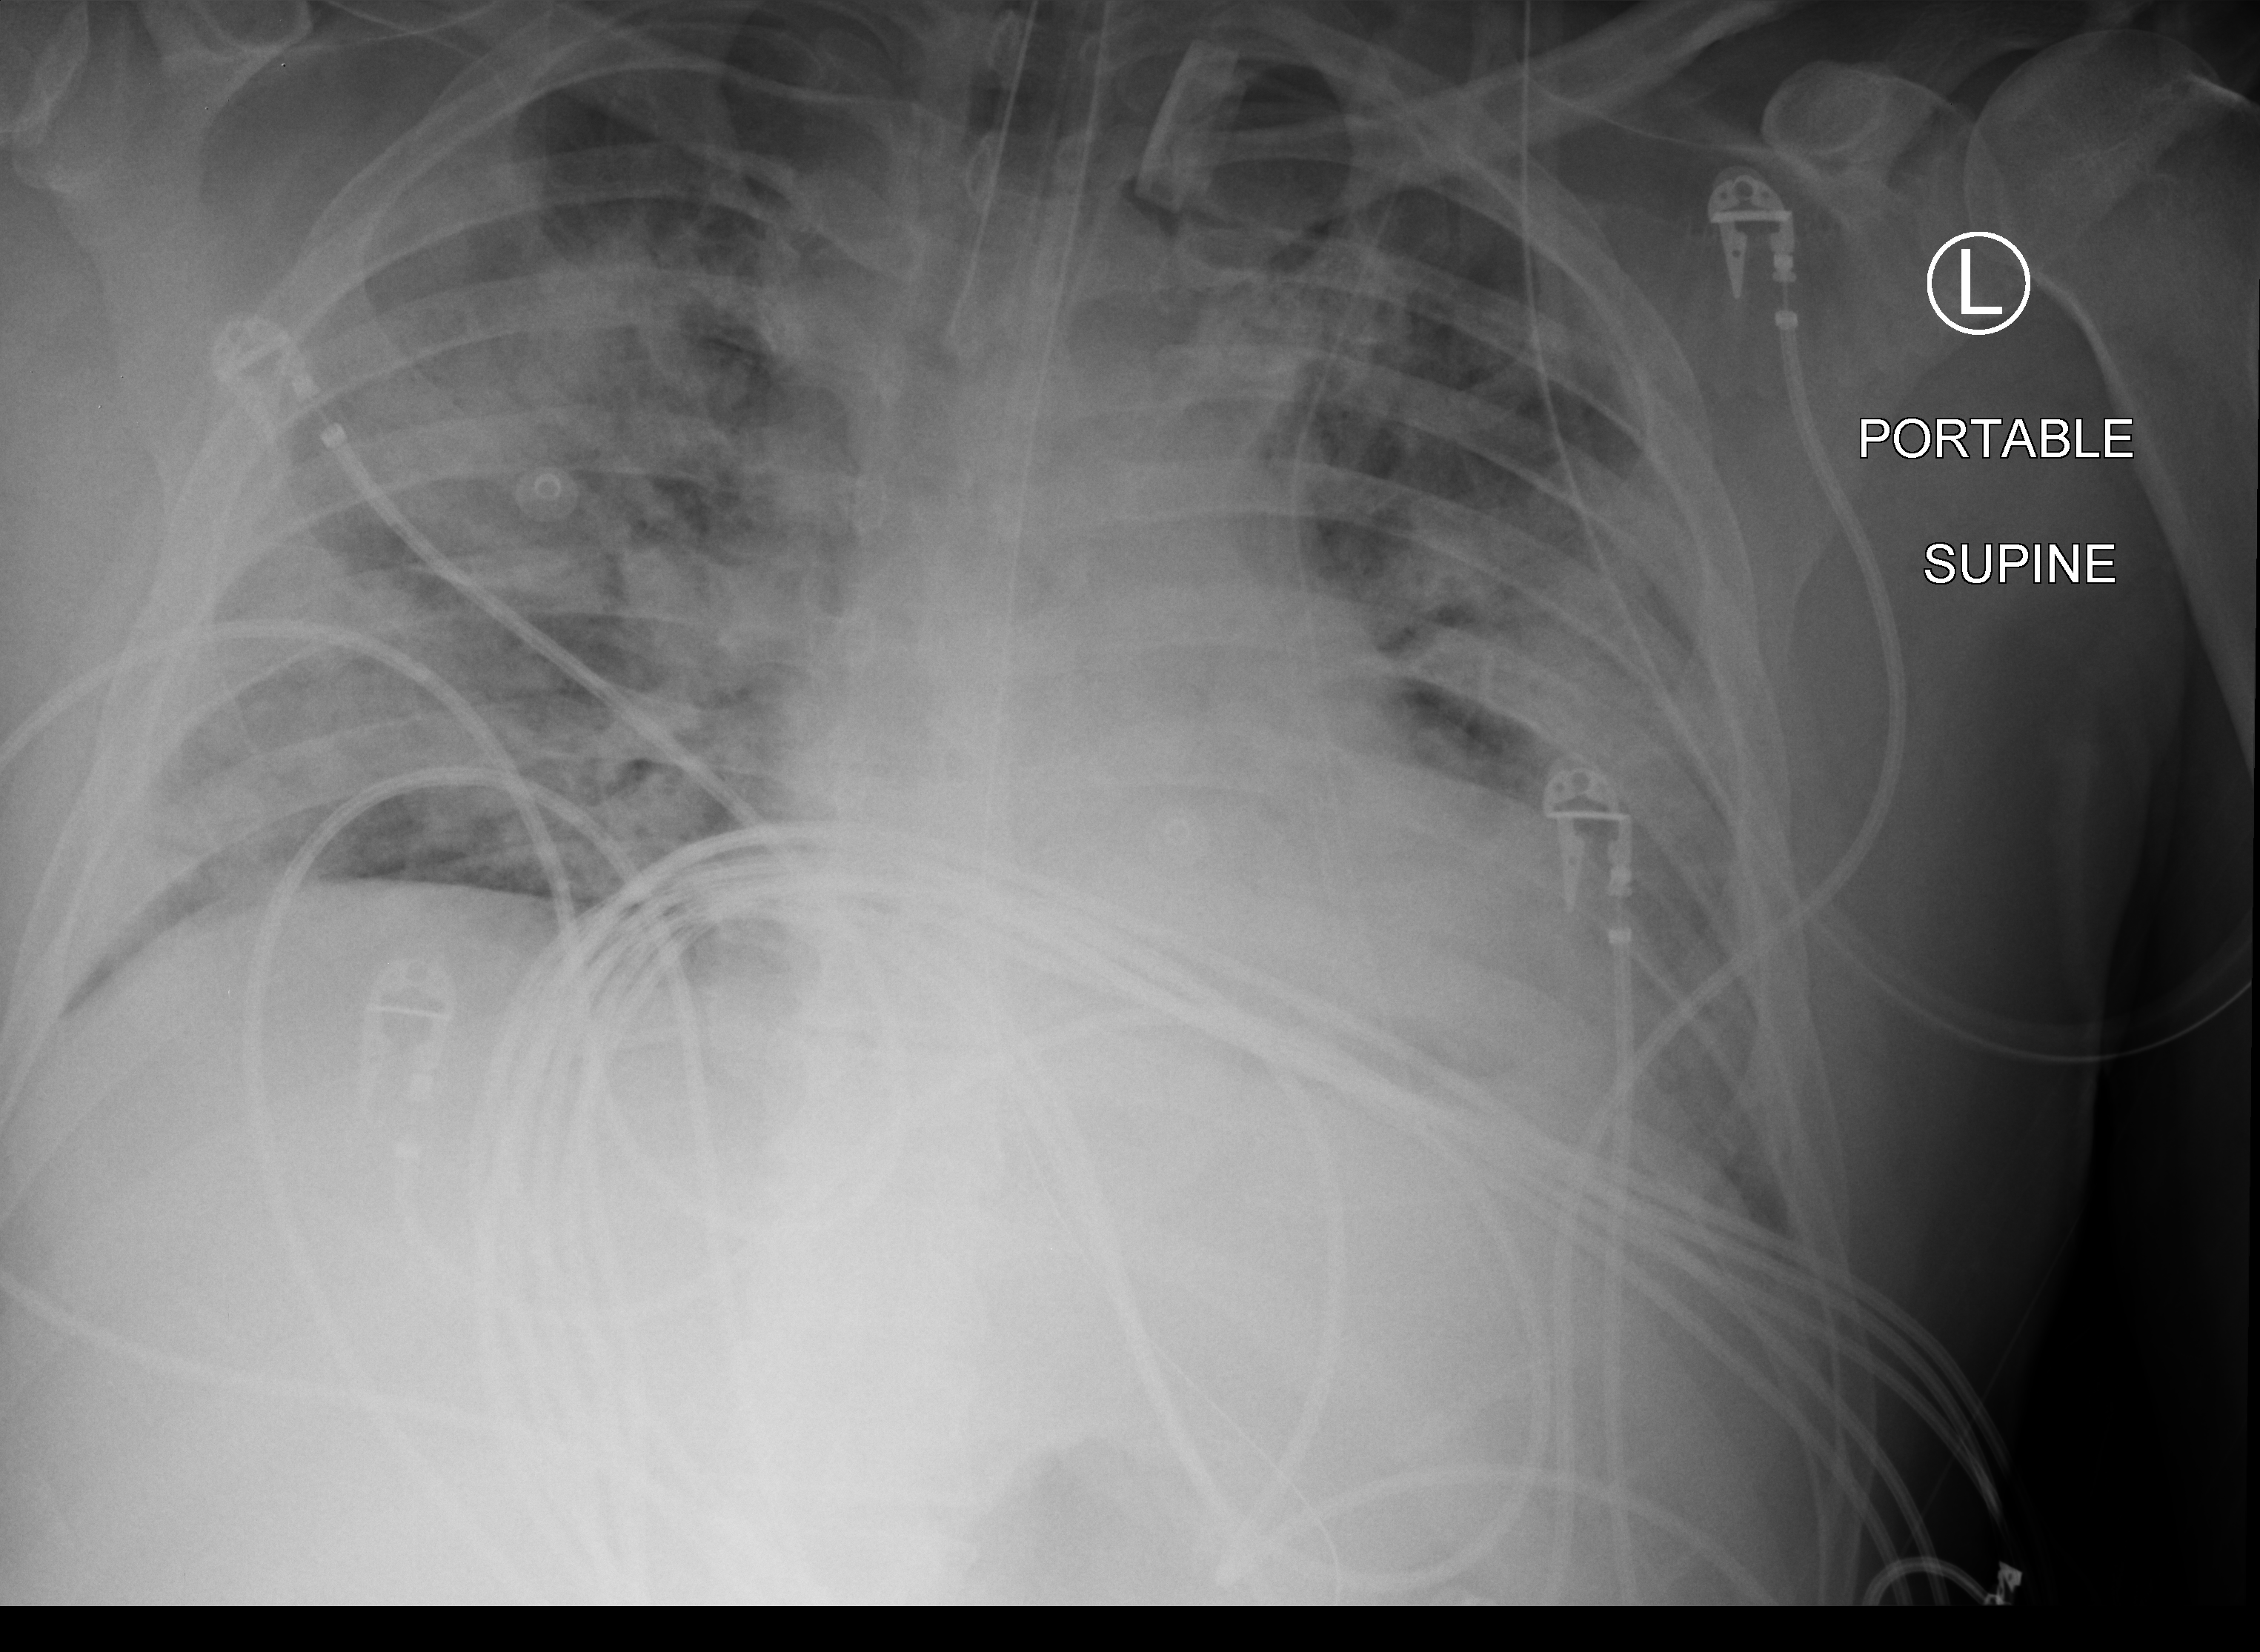
Bedside chest radiograph (computed radiography). Male patient hospitalised with COVID-19, age 18–59 years.
From the hospital-stay record, not from the radiograph (when in the stay this image was taken is not recorded): length of hospital stay: 30 days; chronic kidney disease (admission record): no.